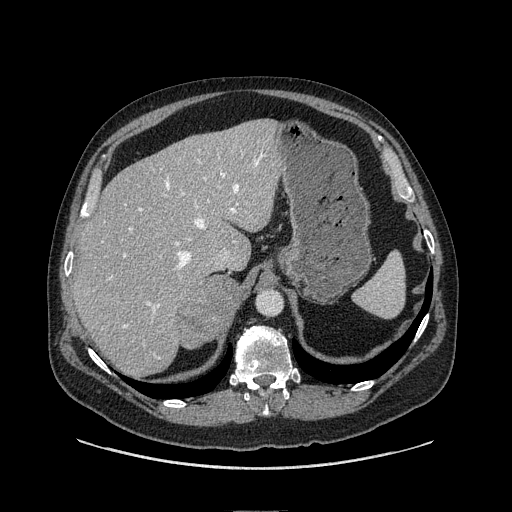
Contrast-enhanced abdominal CT, one axial slice; position 79 of 149 along the scan axis; soft-tissue window (W 400 / L 40 HU); 512 × 512 image matrix, field of view 440 × 440 mm. Male patient. From the clinical record (not read from this slice): diagnosis: adrenocortical carcinoma; tumour side: right adrenal; tumour size at pathology: 7.5 cm; Ki-67 index: 15 %; stage (as recorded): 2.
Annotated regions visible in this slice (semi-automatically segmented with operator editing):
- mass: bounding box <180,274,241,346> (left, top, right, bottom; pixels)